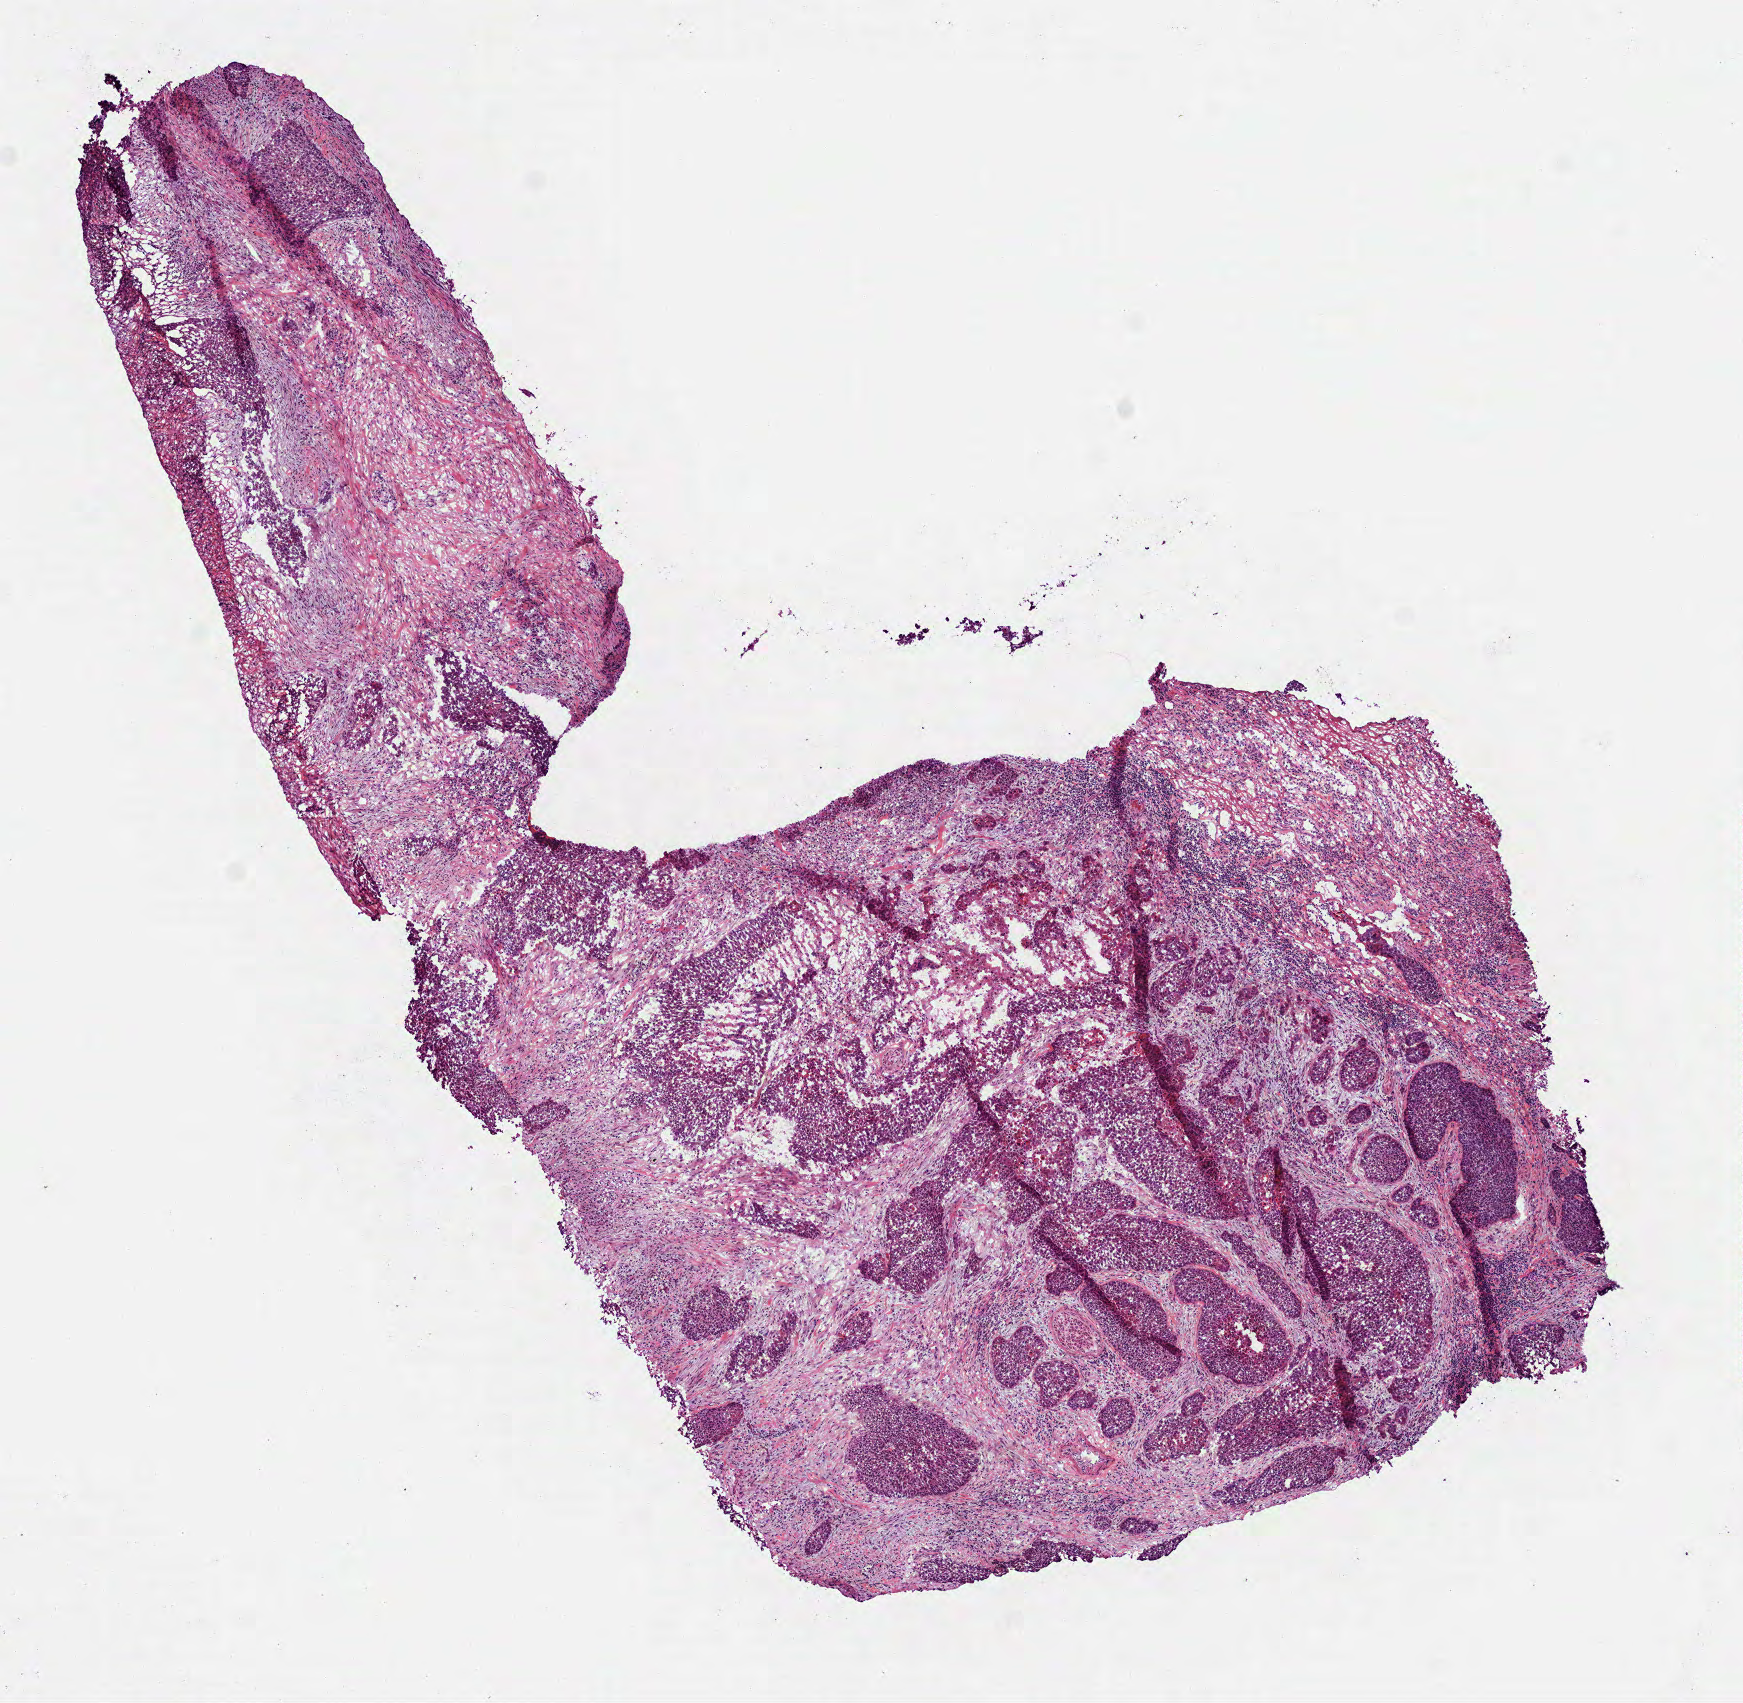
Whole-slide histology image, H&E — whole scanned area (about 7.0 x 6.9 mm, from a 40x scan) shown as a low-resolution overview. Frozen section from the top of the tissue portion. Head and neck, primary tumour sample. Male, age 66 years at initial diagnosis. Histologic grade: G3 (poorly differentiated). Composition of this section per pathologist review: tumour cells 60%, tumour nuclei 60%, normal cells 0%, stromal cells 40%, necrosis 10%.
AJCC pathologic stage: IVA (7th edition). Lymph nodes positive (case pathology): 2 of 25 examined. TNM: T3 N2c. Histologic diagnosis: Squamous cell carcinoma, NOS (larynx, NOS).